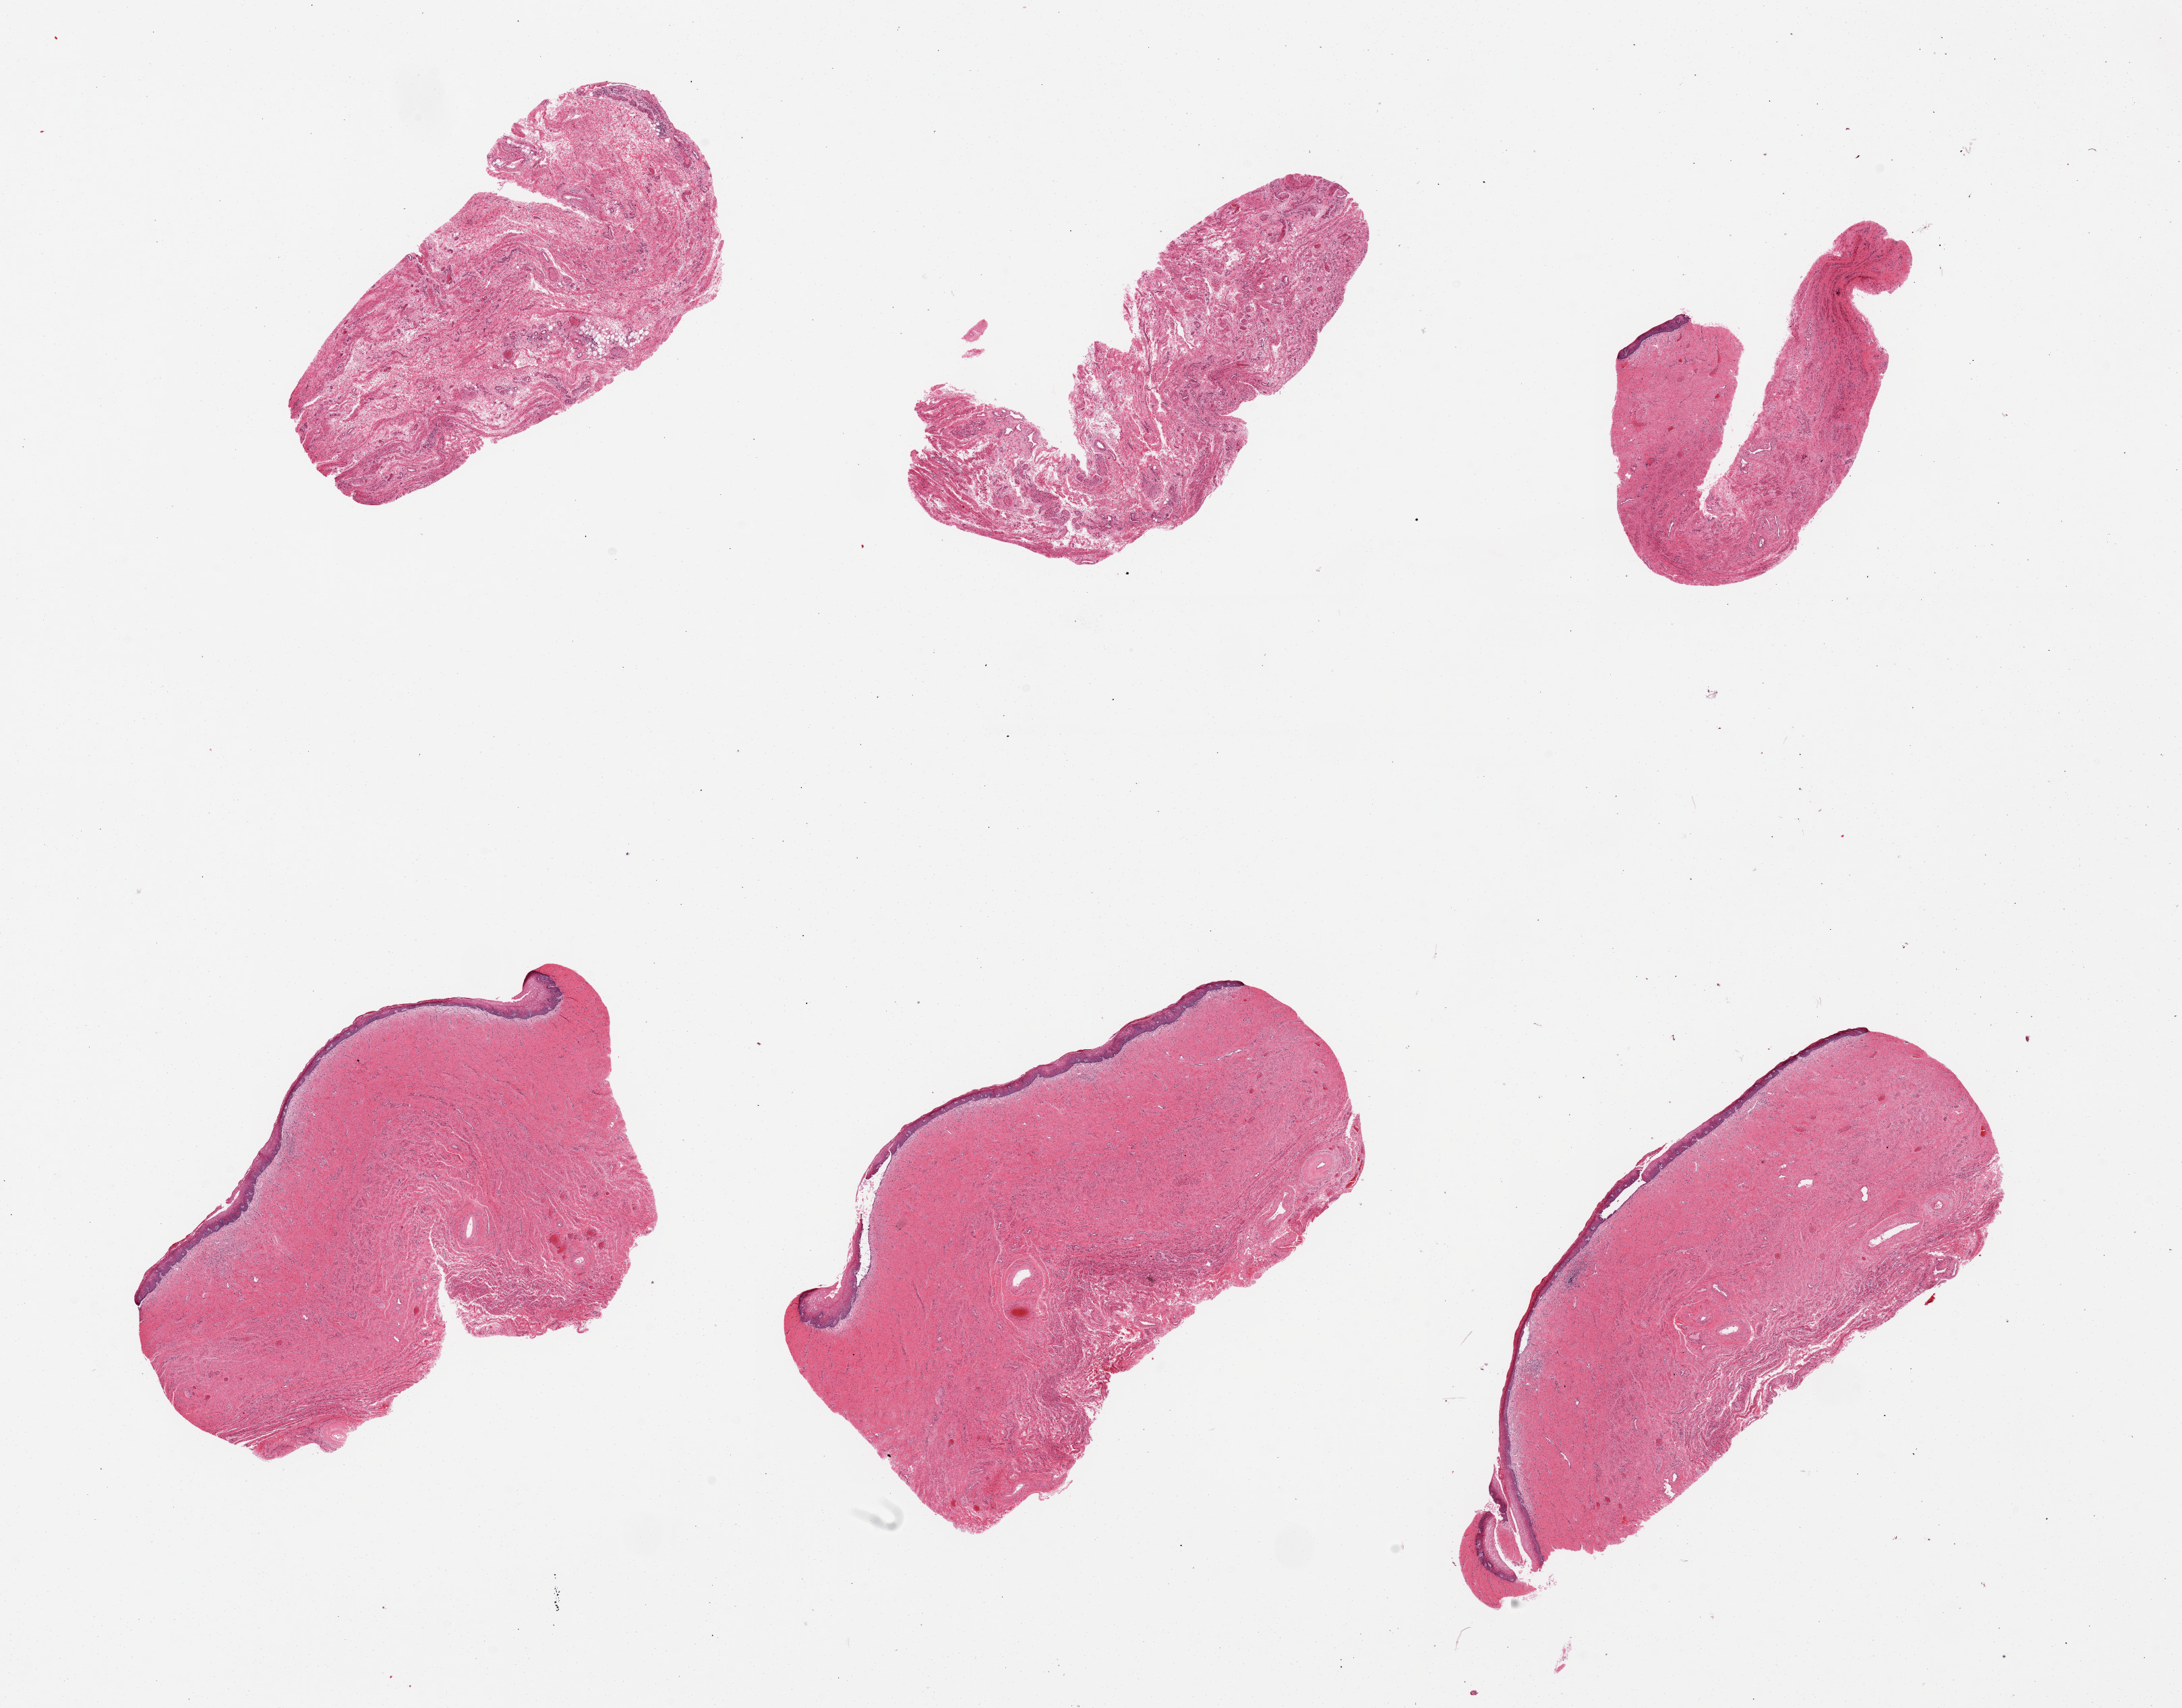
Haematoxylin and eosin whole-slide image — a low-resolution overview of the entire scanned area, about 25.6 x 20.0 mm. PAXgene-fixed paraffin-embedded (PFPE) section. Sampled site (target tissue): vagina. Donor tissue sample. Donor sex: female.
Reviewer comment on this tissue sample: 6 pieces, squamous epithelium is ~ 2-3% thickness, partially sloughing.